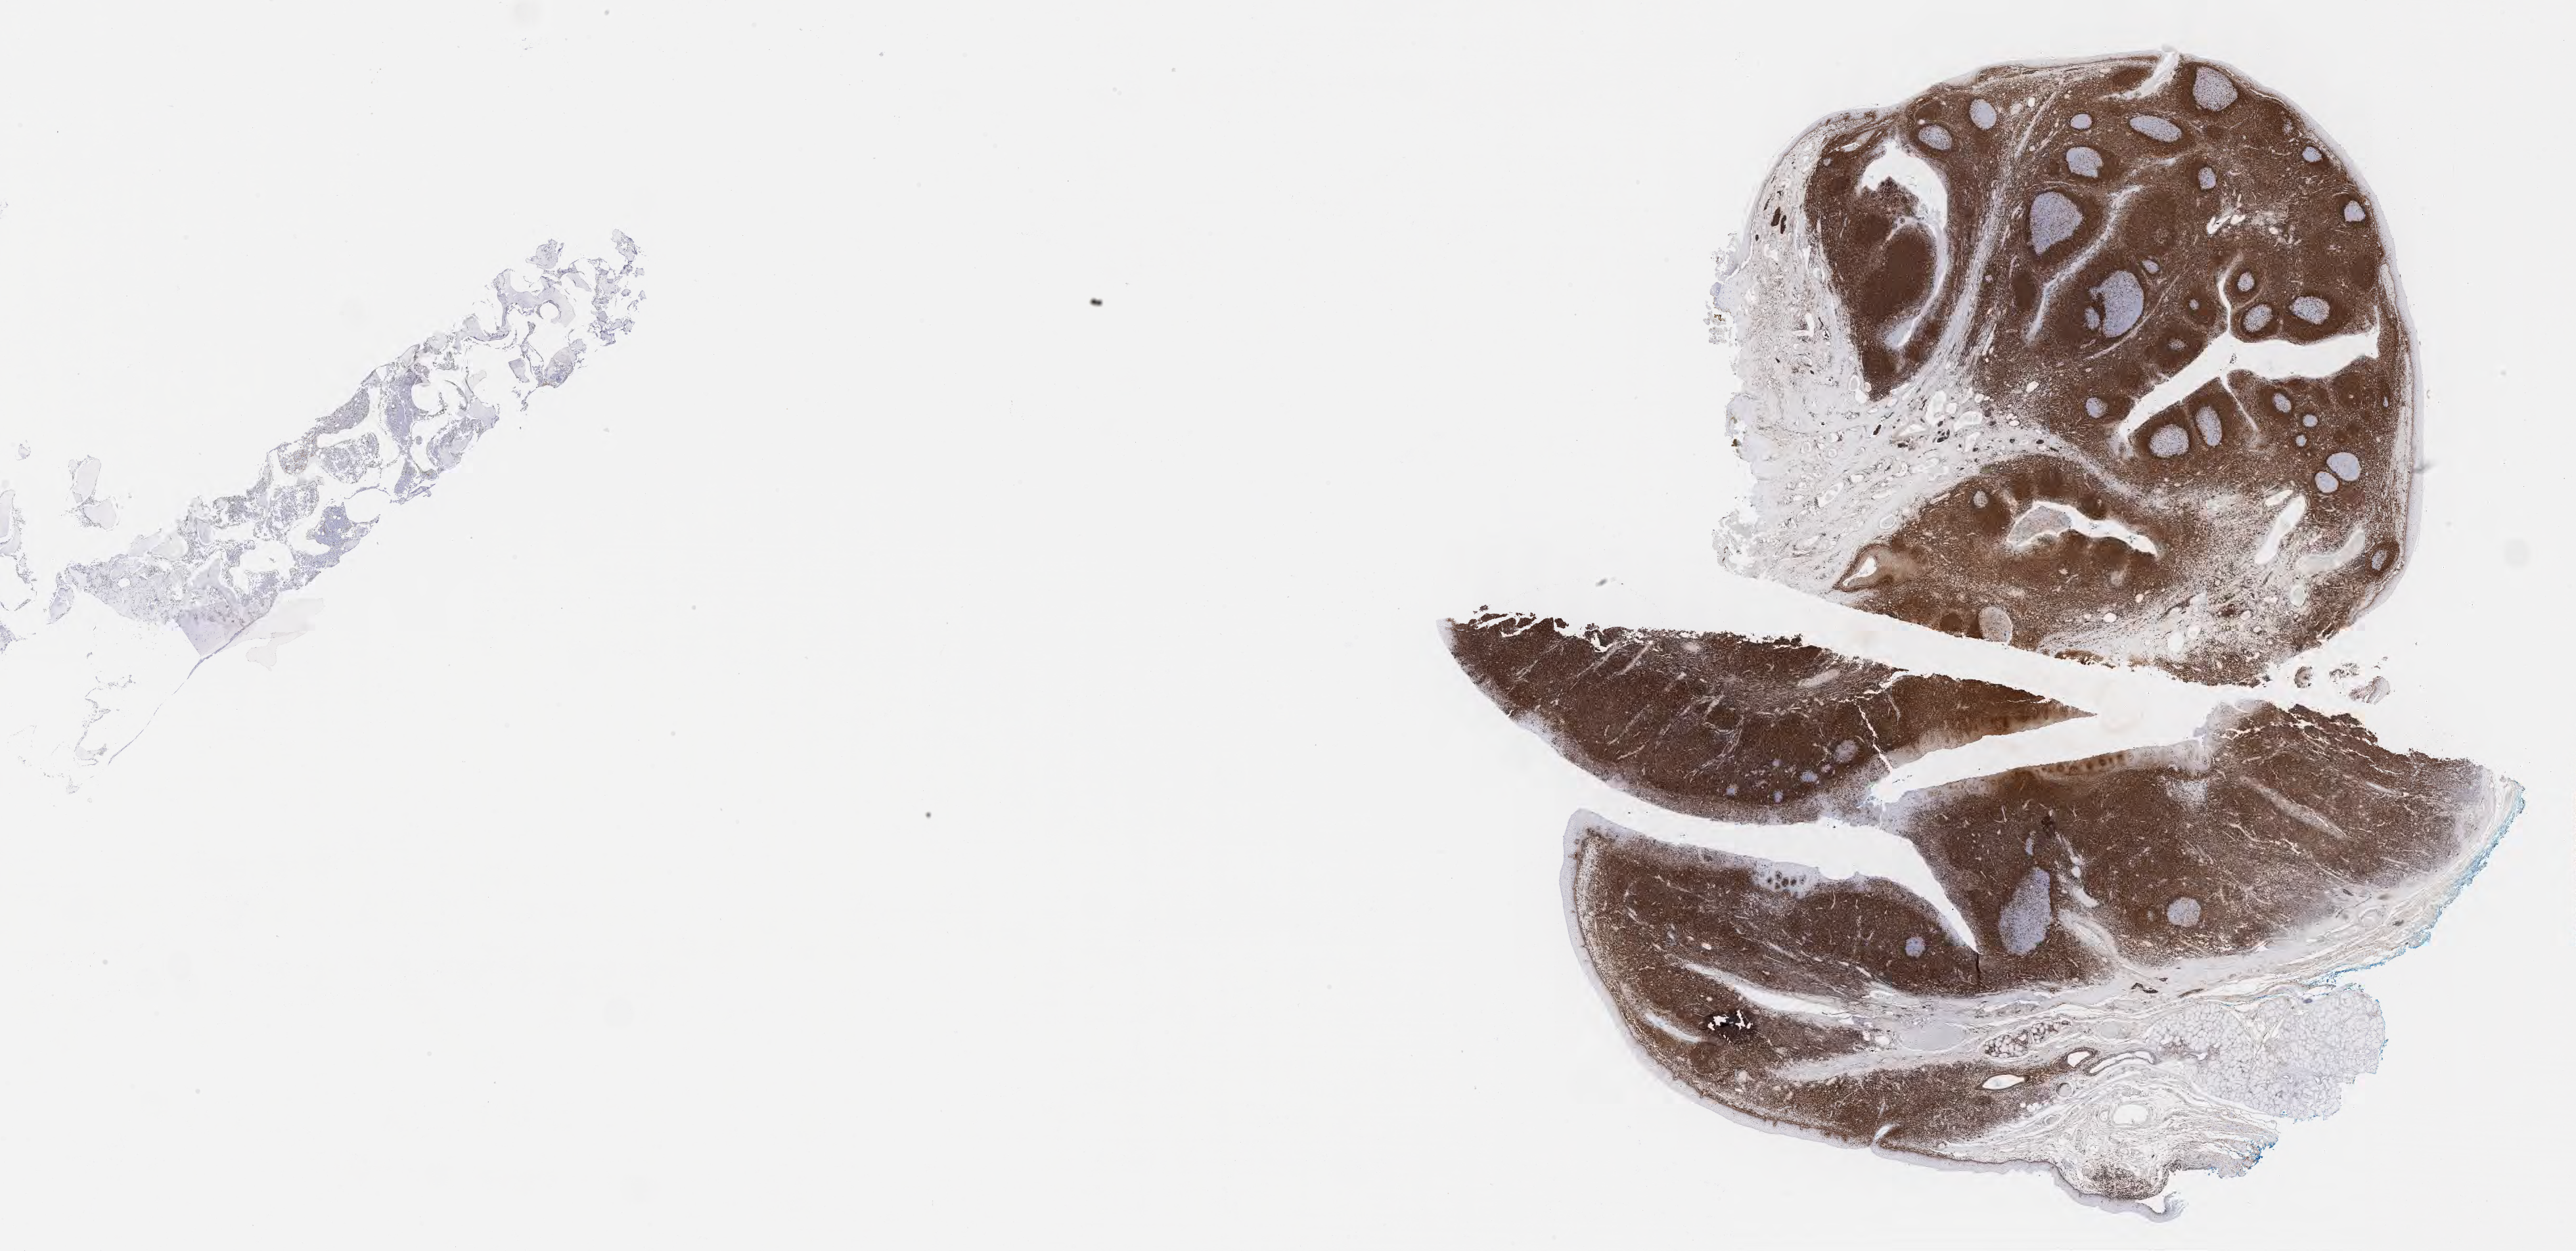
Whole-slide image, immunohistochemical stain for BCL2 — low-resolution overview of the scanned area, about 31.7 x 15.4 mm, tumor tissue. Patient male; age 13 years.
Diagnosis: Burkitt lymphoma, NOS.